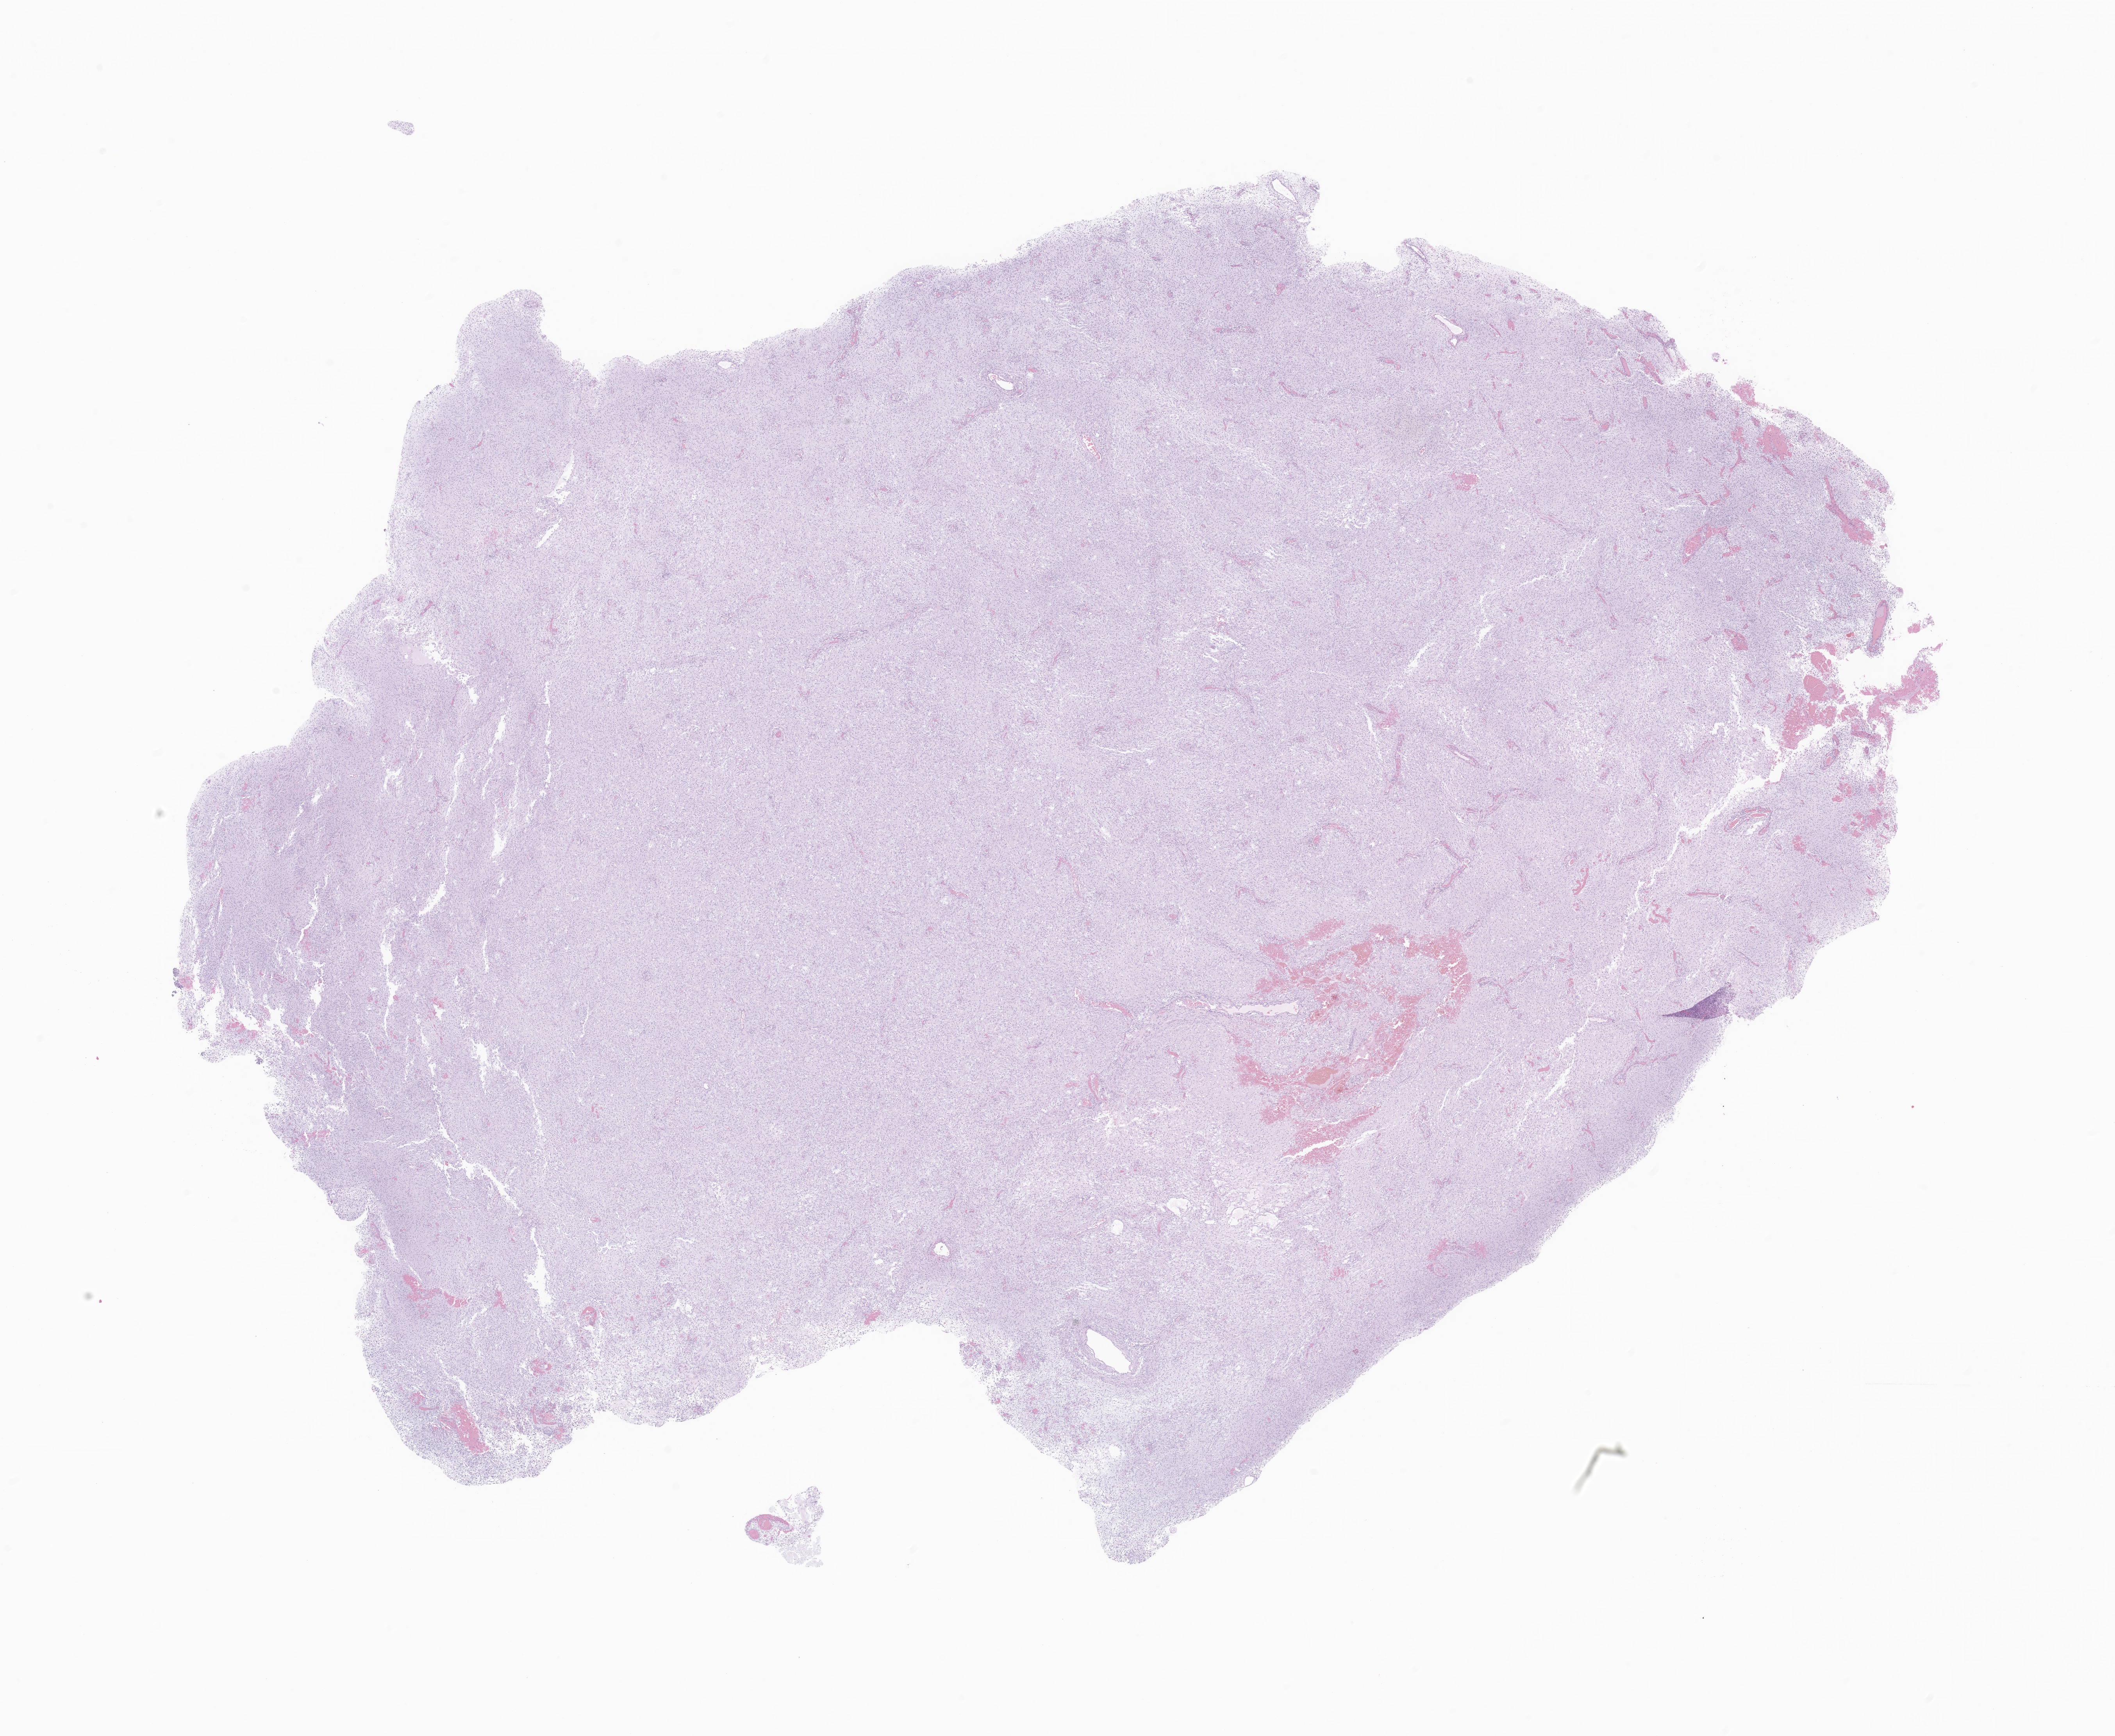
Digitized haematoxylin and eosin-stained section of tumor tissue from the brain, a low-resolution overview of the entire scanned area, about 22.8 x 18.7 mm, formalin-fixed, paraffin-embedded (FFPE) tissue. Patient female; age 722 days (about 2.0 years).
Recorded diagnosis: Neoplasm, malignant.